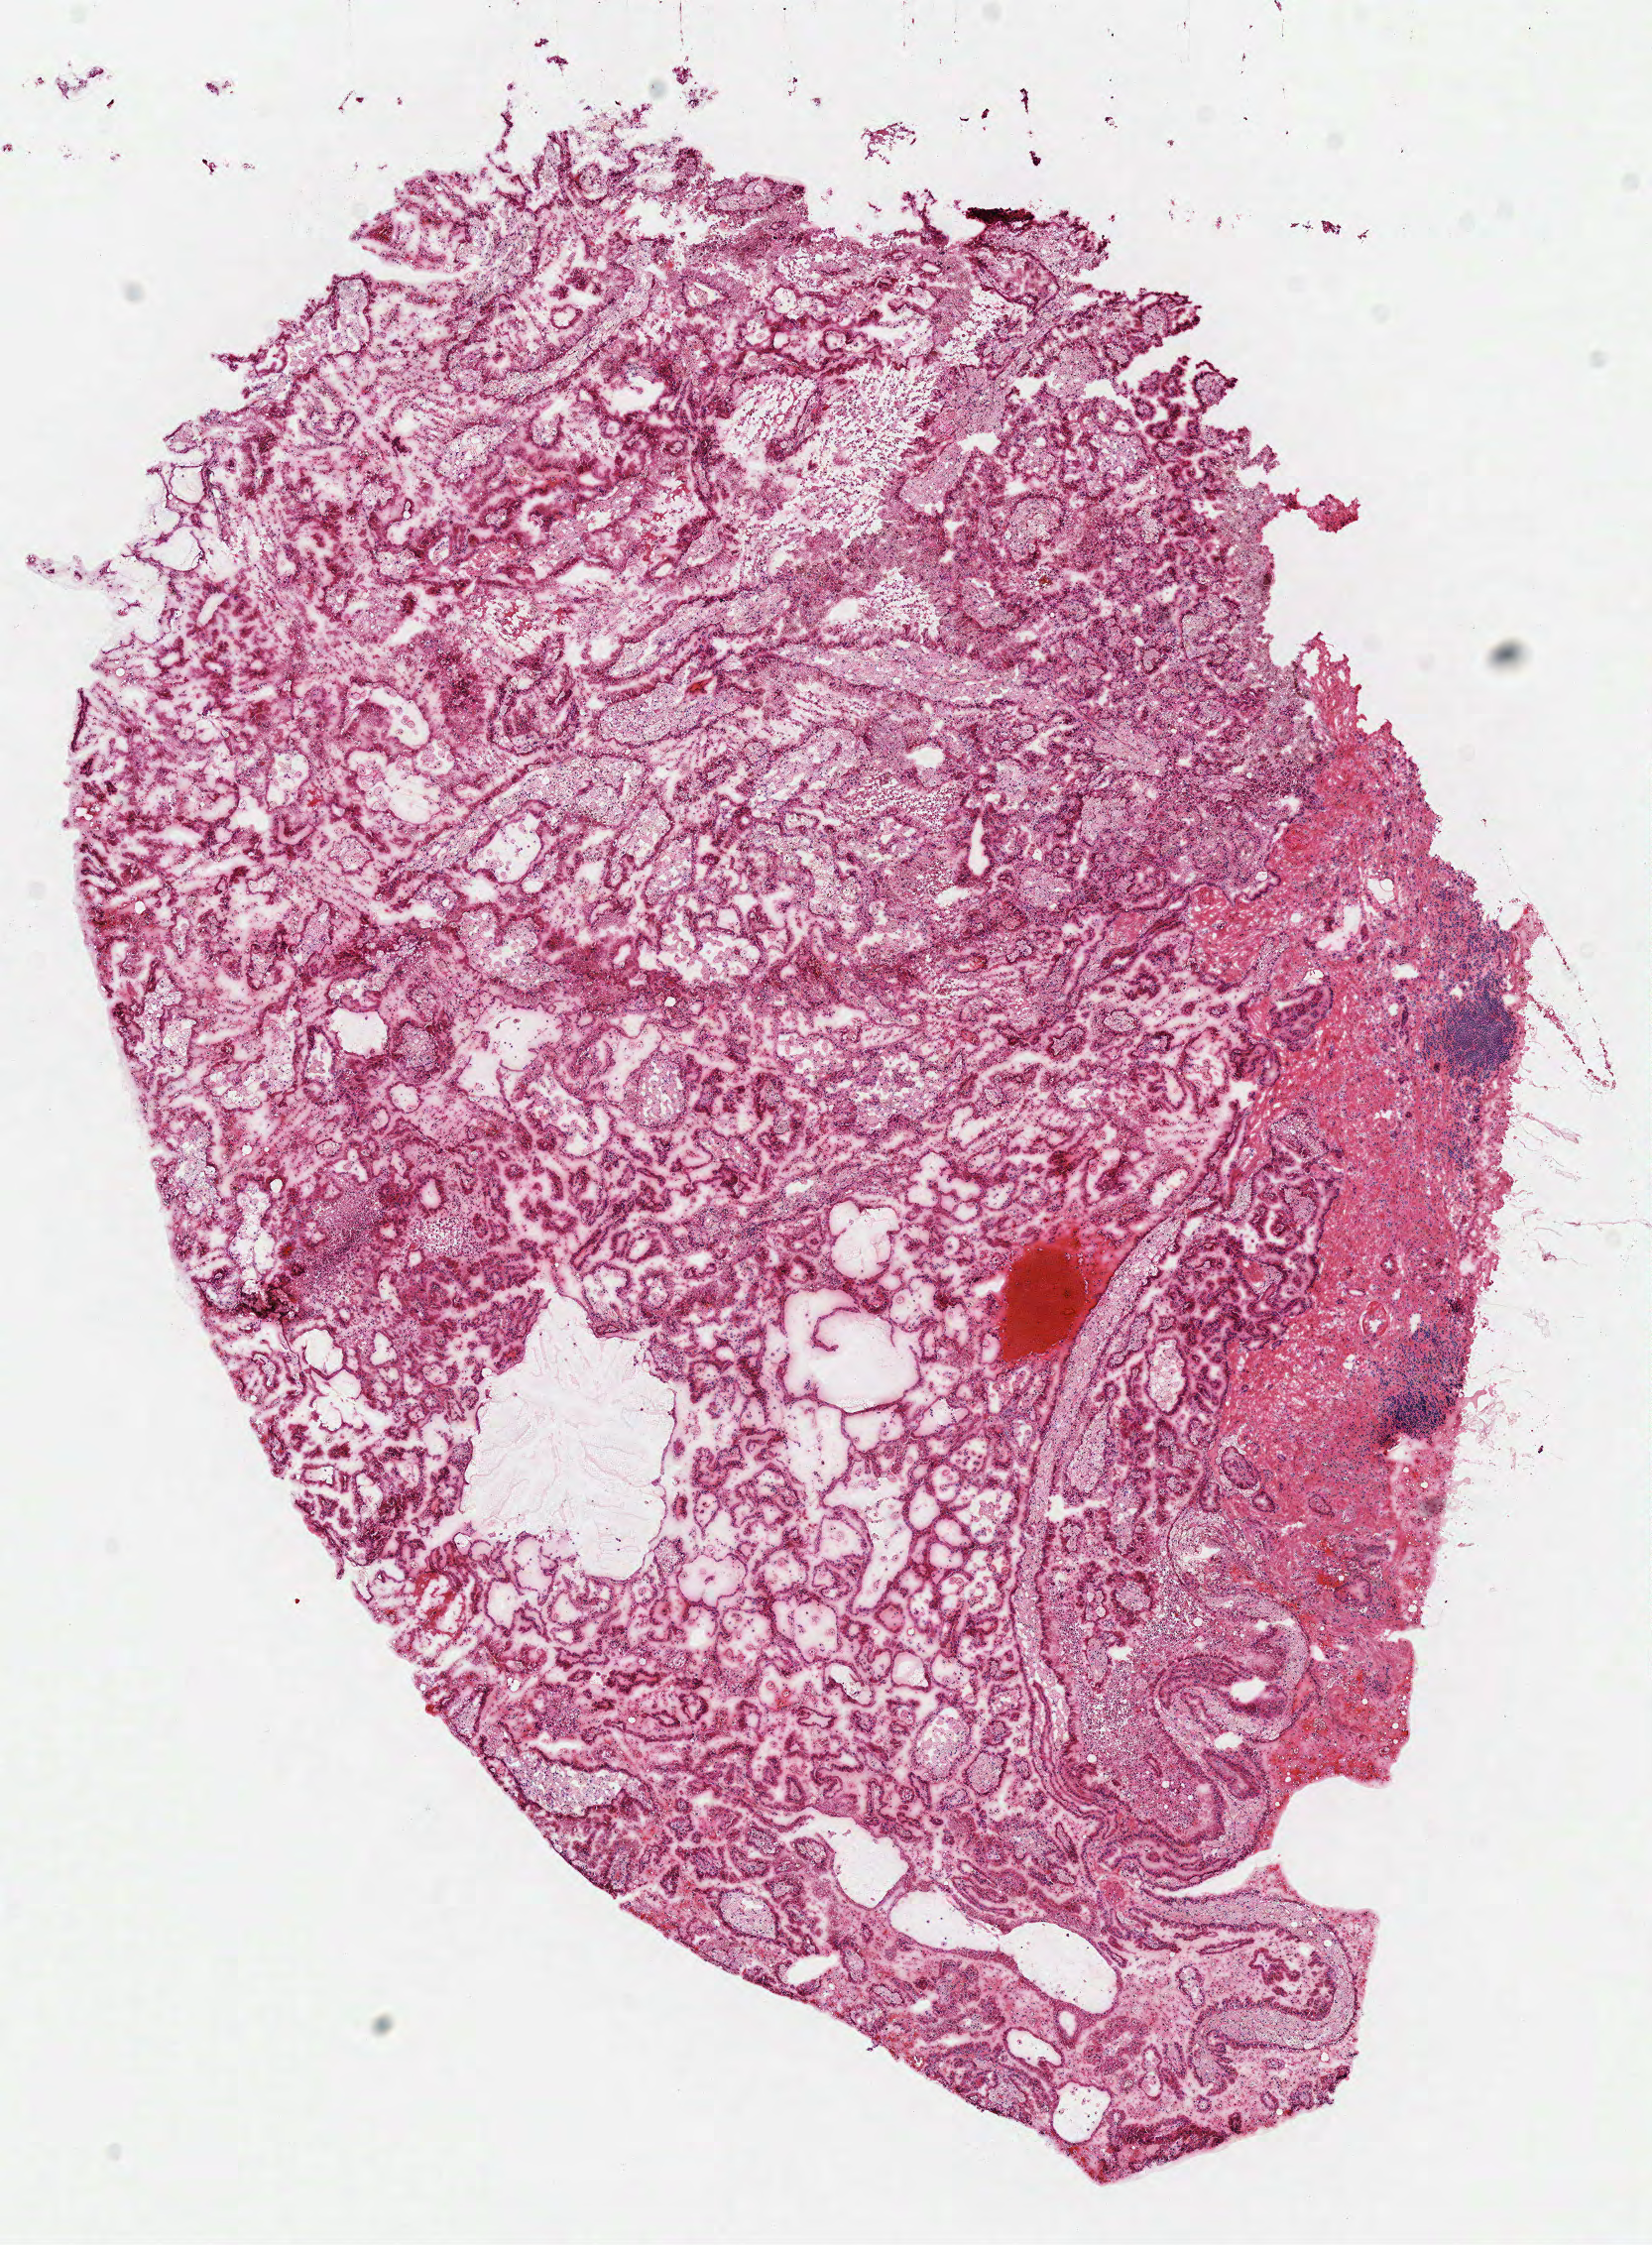
Digitized Hematoxylin and eosin (H&E) stained tissue section (whole slide) — shown as a low-resolution overview of the whole scanned area (about 6.6 x 8.9 mm, acquisition: 40x scan). Frozen section. Sample: primary tumour, kidney. Male patient; age at initial diagnosis 69 years. Pathologist review of this section (percent, as recorded): tumour cells 72%, tumour nuclei 75%, normal cells 0%, stromal cells 25%, necrosis 3%. Inflammatory infiltration, as recorded: lymphocyte infiltration 10%, monocyte infiltration 10%, neutrophil infiltration 0%.
* AJCC pathologic stage: I
* laterality: left
* pathologic diagnosis: Papillary adenocarcinoma, NOS